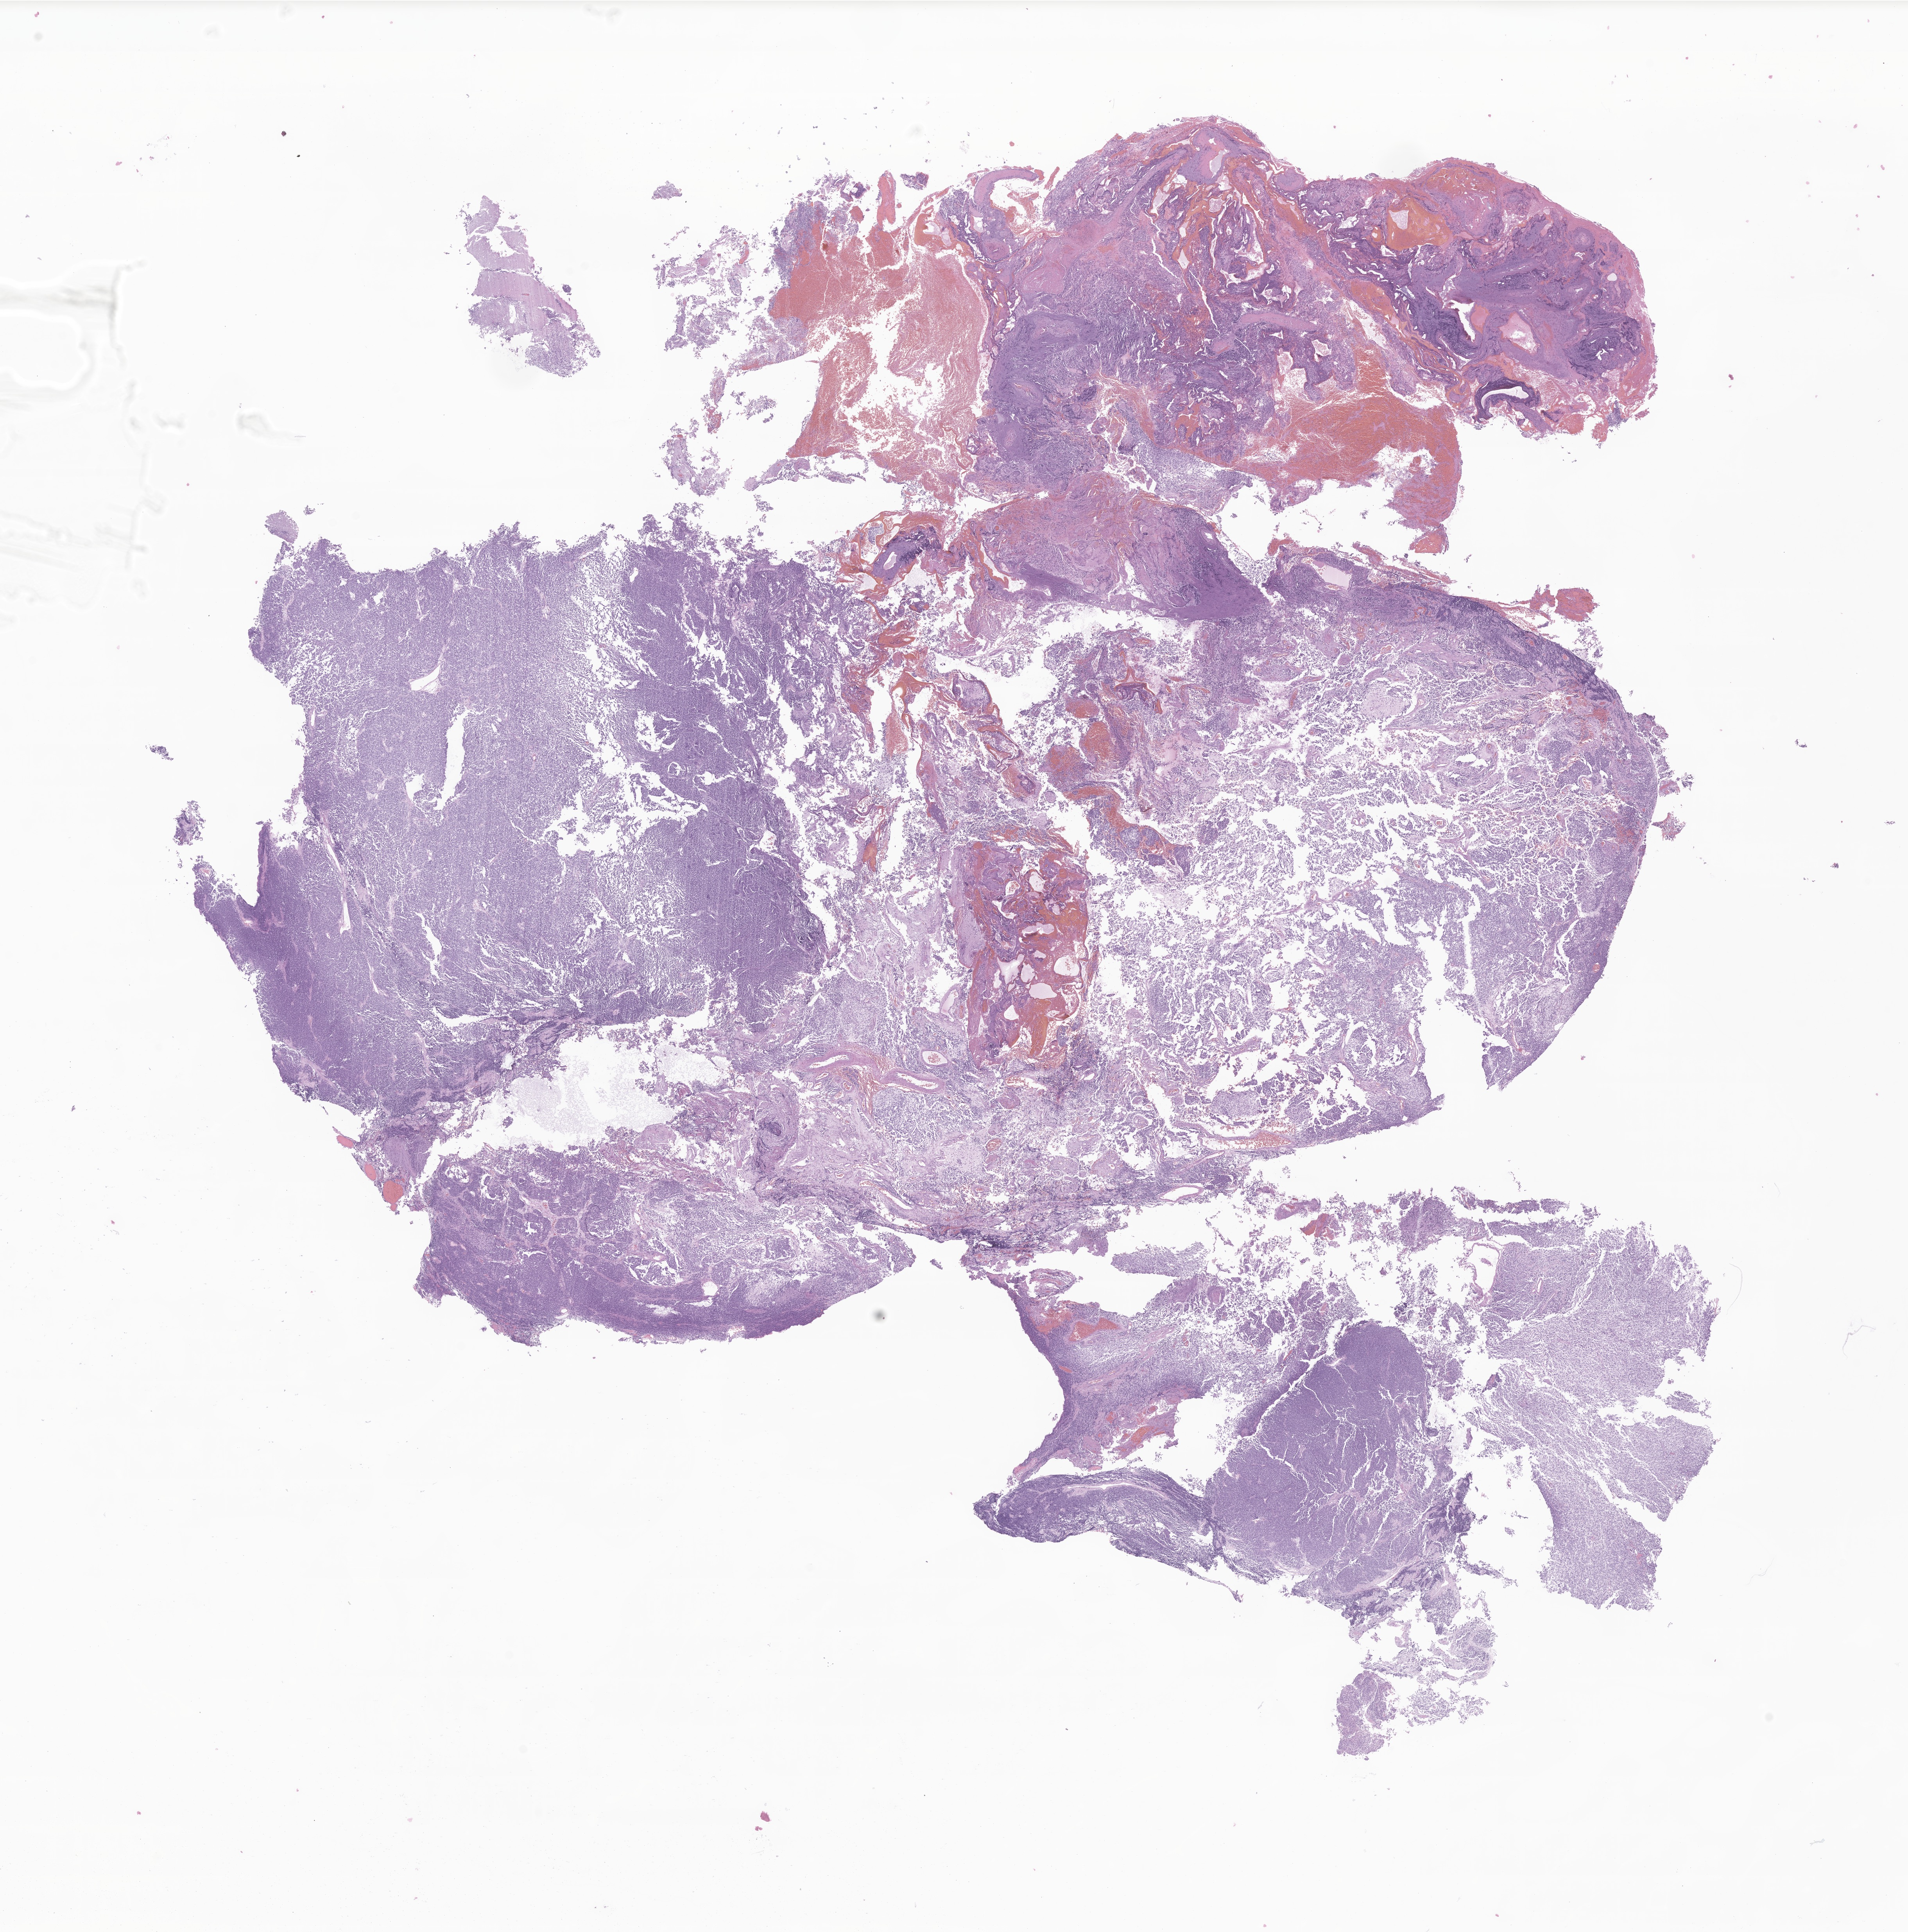
Digitized haematoxylin and eosin-stained section of tumor tissue from the brain — low-resolution overview of the scanned area, about 20.6 x 20.8 mm. FFPE section. Patient: female, age 102 months.
Recorded diagnosis: Medulloblastoma, NOS.